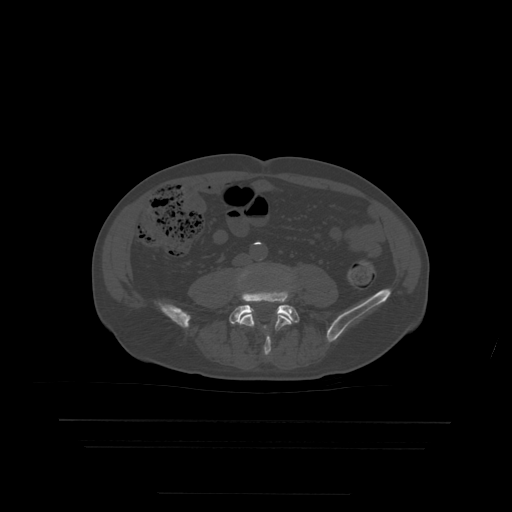
CT including the spine, one axial slice; slice 84 of 522 in the series (ordered by position); bone window (W 1800 / L 400 HU); 1.25 mm slice thickness; 512 × 512 image matrix, field of view 436 × 436 mm. Patient age 68 years. Case-level facts recorded for this patient, not image findings: primary cancer: urothelial.
Outlined on this slice (semi-automatic segmentation, software-assisted and operator-edited):
- L4 vertebra: bounding box (x1, y1, x2, y2) in pixels: (238, 269, 292, 356)
- L5 vertebra: (229, 292, 300, 324)